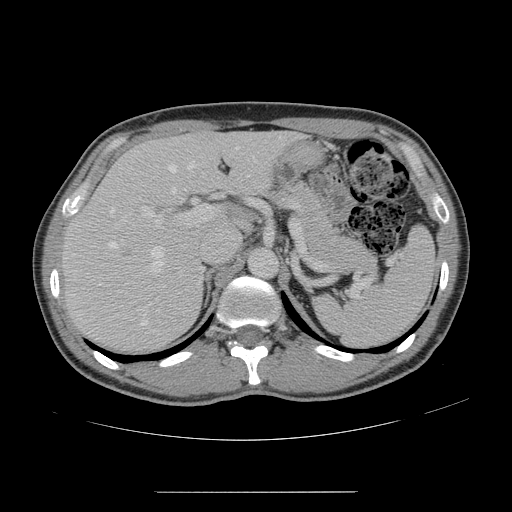
Contrast-enhanced abdominal CT, one axial slice. Position 98 of 178 along the scan axis. Intravenous contrast given. Soft-tissue window (W 400 / L 40 HU). 2.5 mm slice thickness. 512 × 512 image matrix. Male patient, age 53 years. From the clinical record (not read from this slice): diagnosis: colorectal cancer liver metastases, imaged before liver resection; multiple liver metastases: yes; largest metastasis: 2.4 cm; chemotherapy before resection: yes.
Annotated regions visible in this slice (outlined manually by an expert reader):
- hepatic veins: bounding box [x1, y1, x2, y2] px = [109, 147, 238, 326]
- liver: [64, 133, 297, 350]
- planned liver remnant (the part of the liver to remain after resection): [147, 133, 297, 193]
- portal vein (with intrahepatic branches): [142, 205, 214, 227]